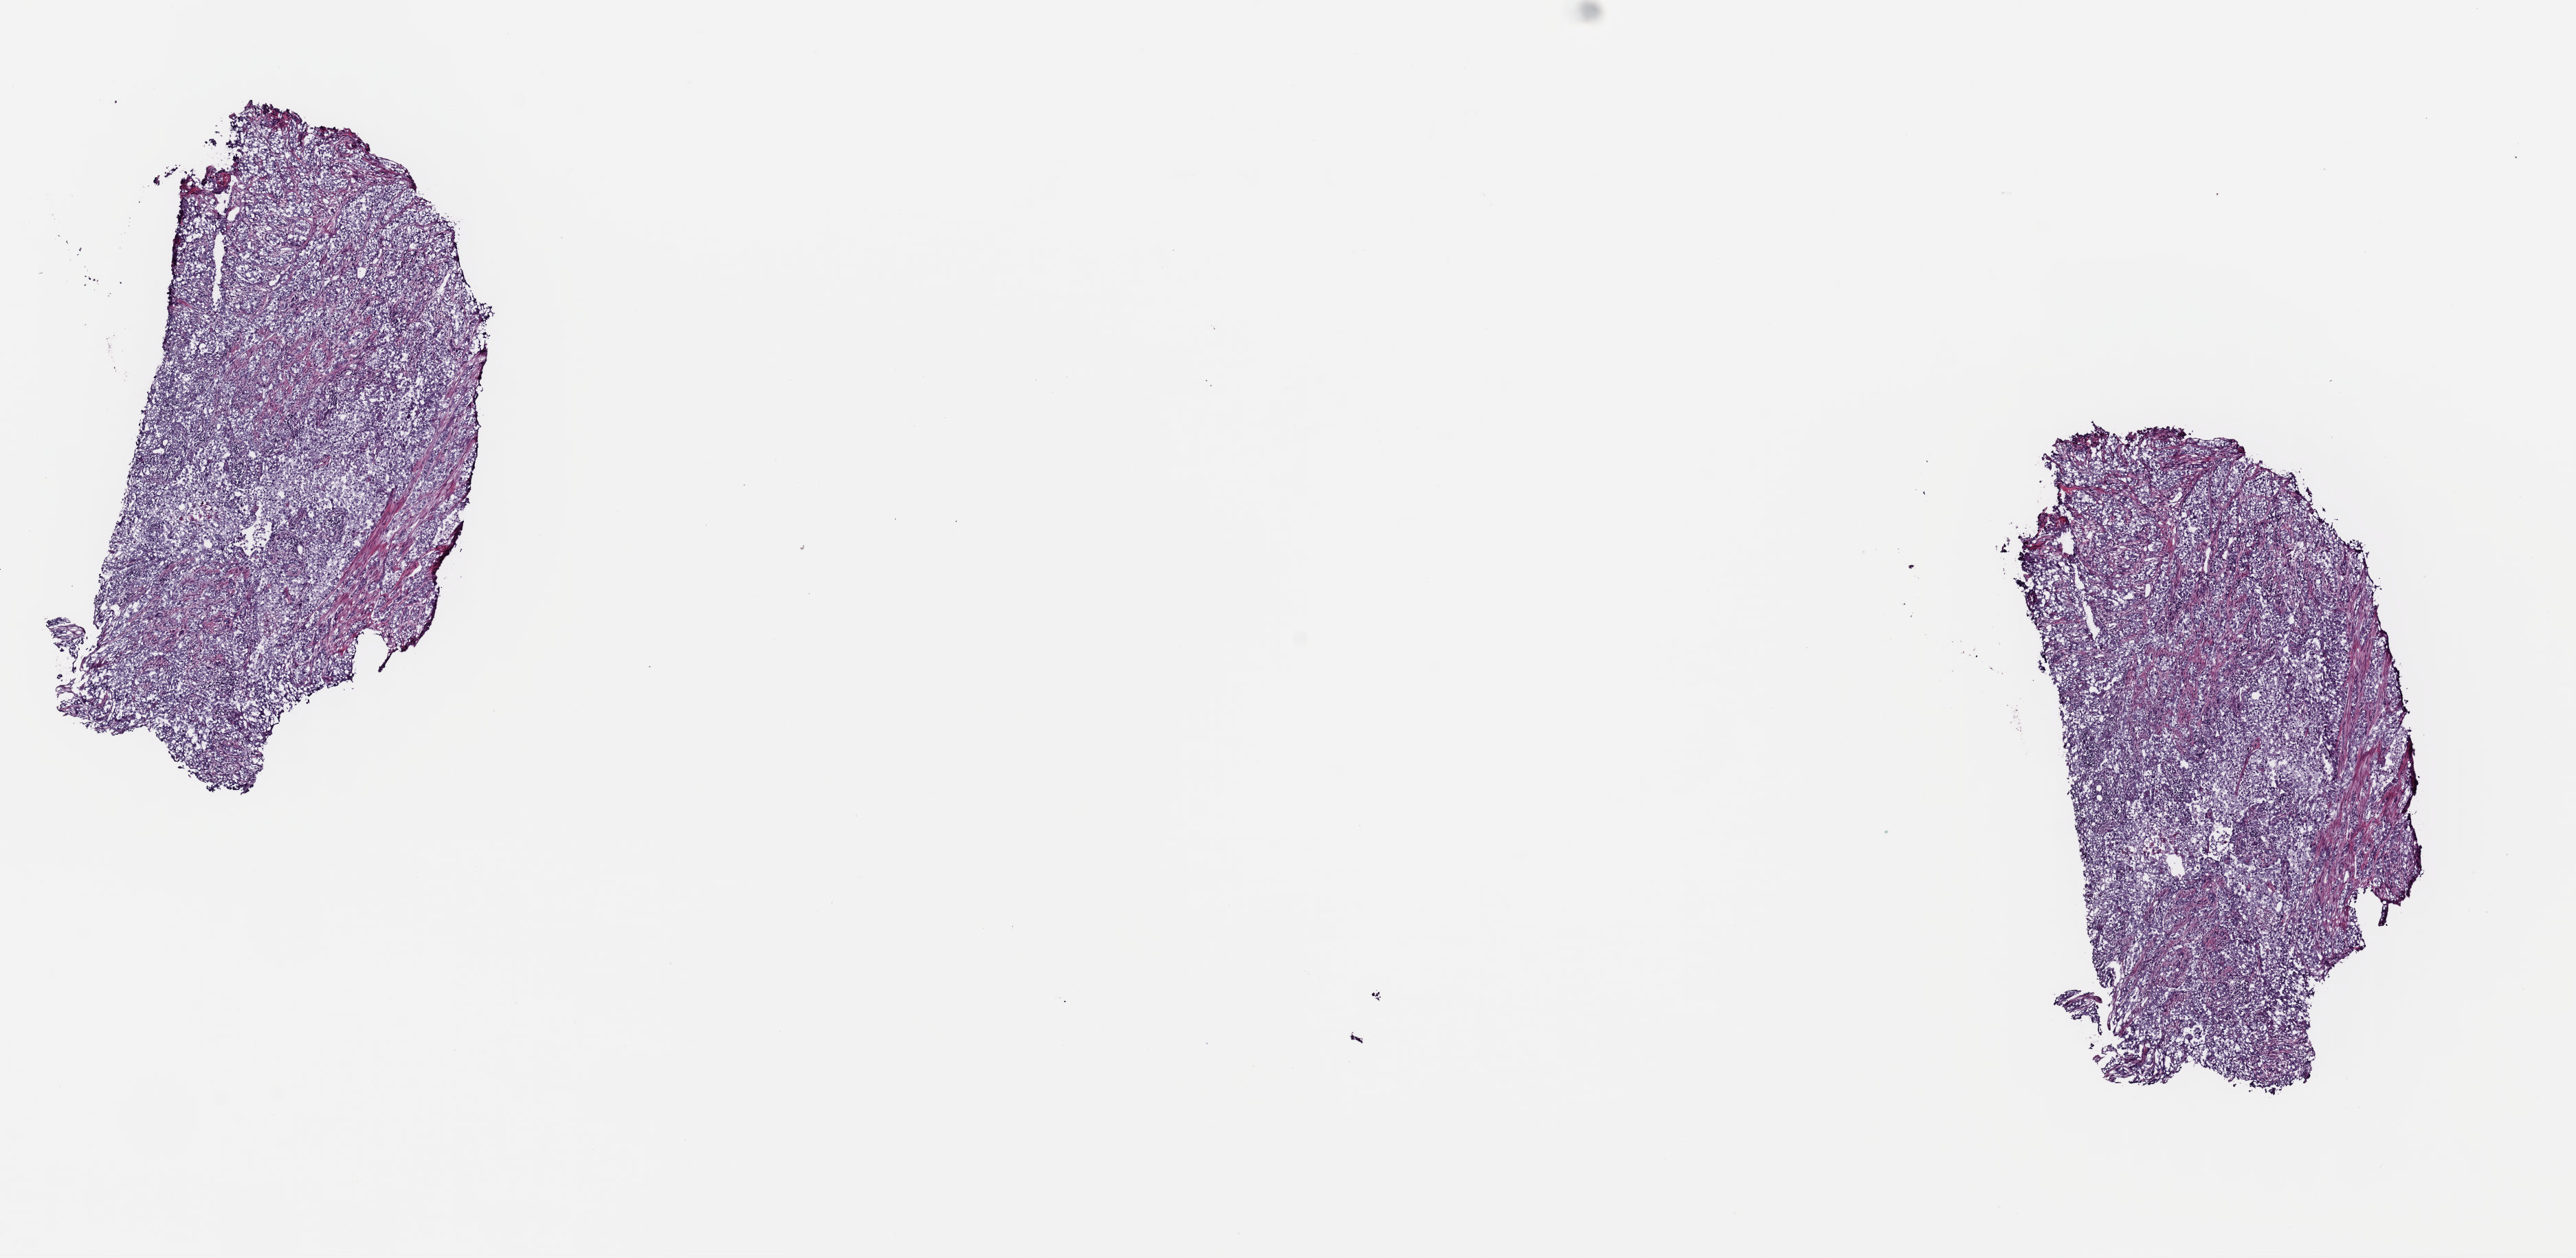
Whole-slide histology image, H&E-stained, shown as a low-resolution overview of the whole scanned area (about 14.8 x 7.2 mm, acquisition: 40x scan), frozen section from the top of the tissue portion, primary tumour sample from the bladder. Male patient; age at initial diagnosis 72 years. Histologic grade: high grade. Composition of this section per pathologist review: tumour cells 90%, tumour nuclei 95%, normal cells 0%, stromal cells 10%, necrosis 0%. Inflammatory infiltration, as recorded: lymphocyte infiltration 0%, monocyte infiltration 0%, neutrophil infiltration 0%.
Pathologic diagnosis: Transitional cell carcinoma (lateral wall of bladder). AJCC pathologic stage: III (7th edition).